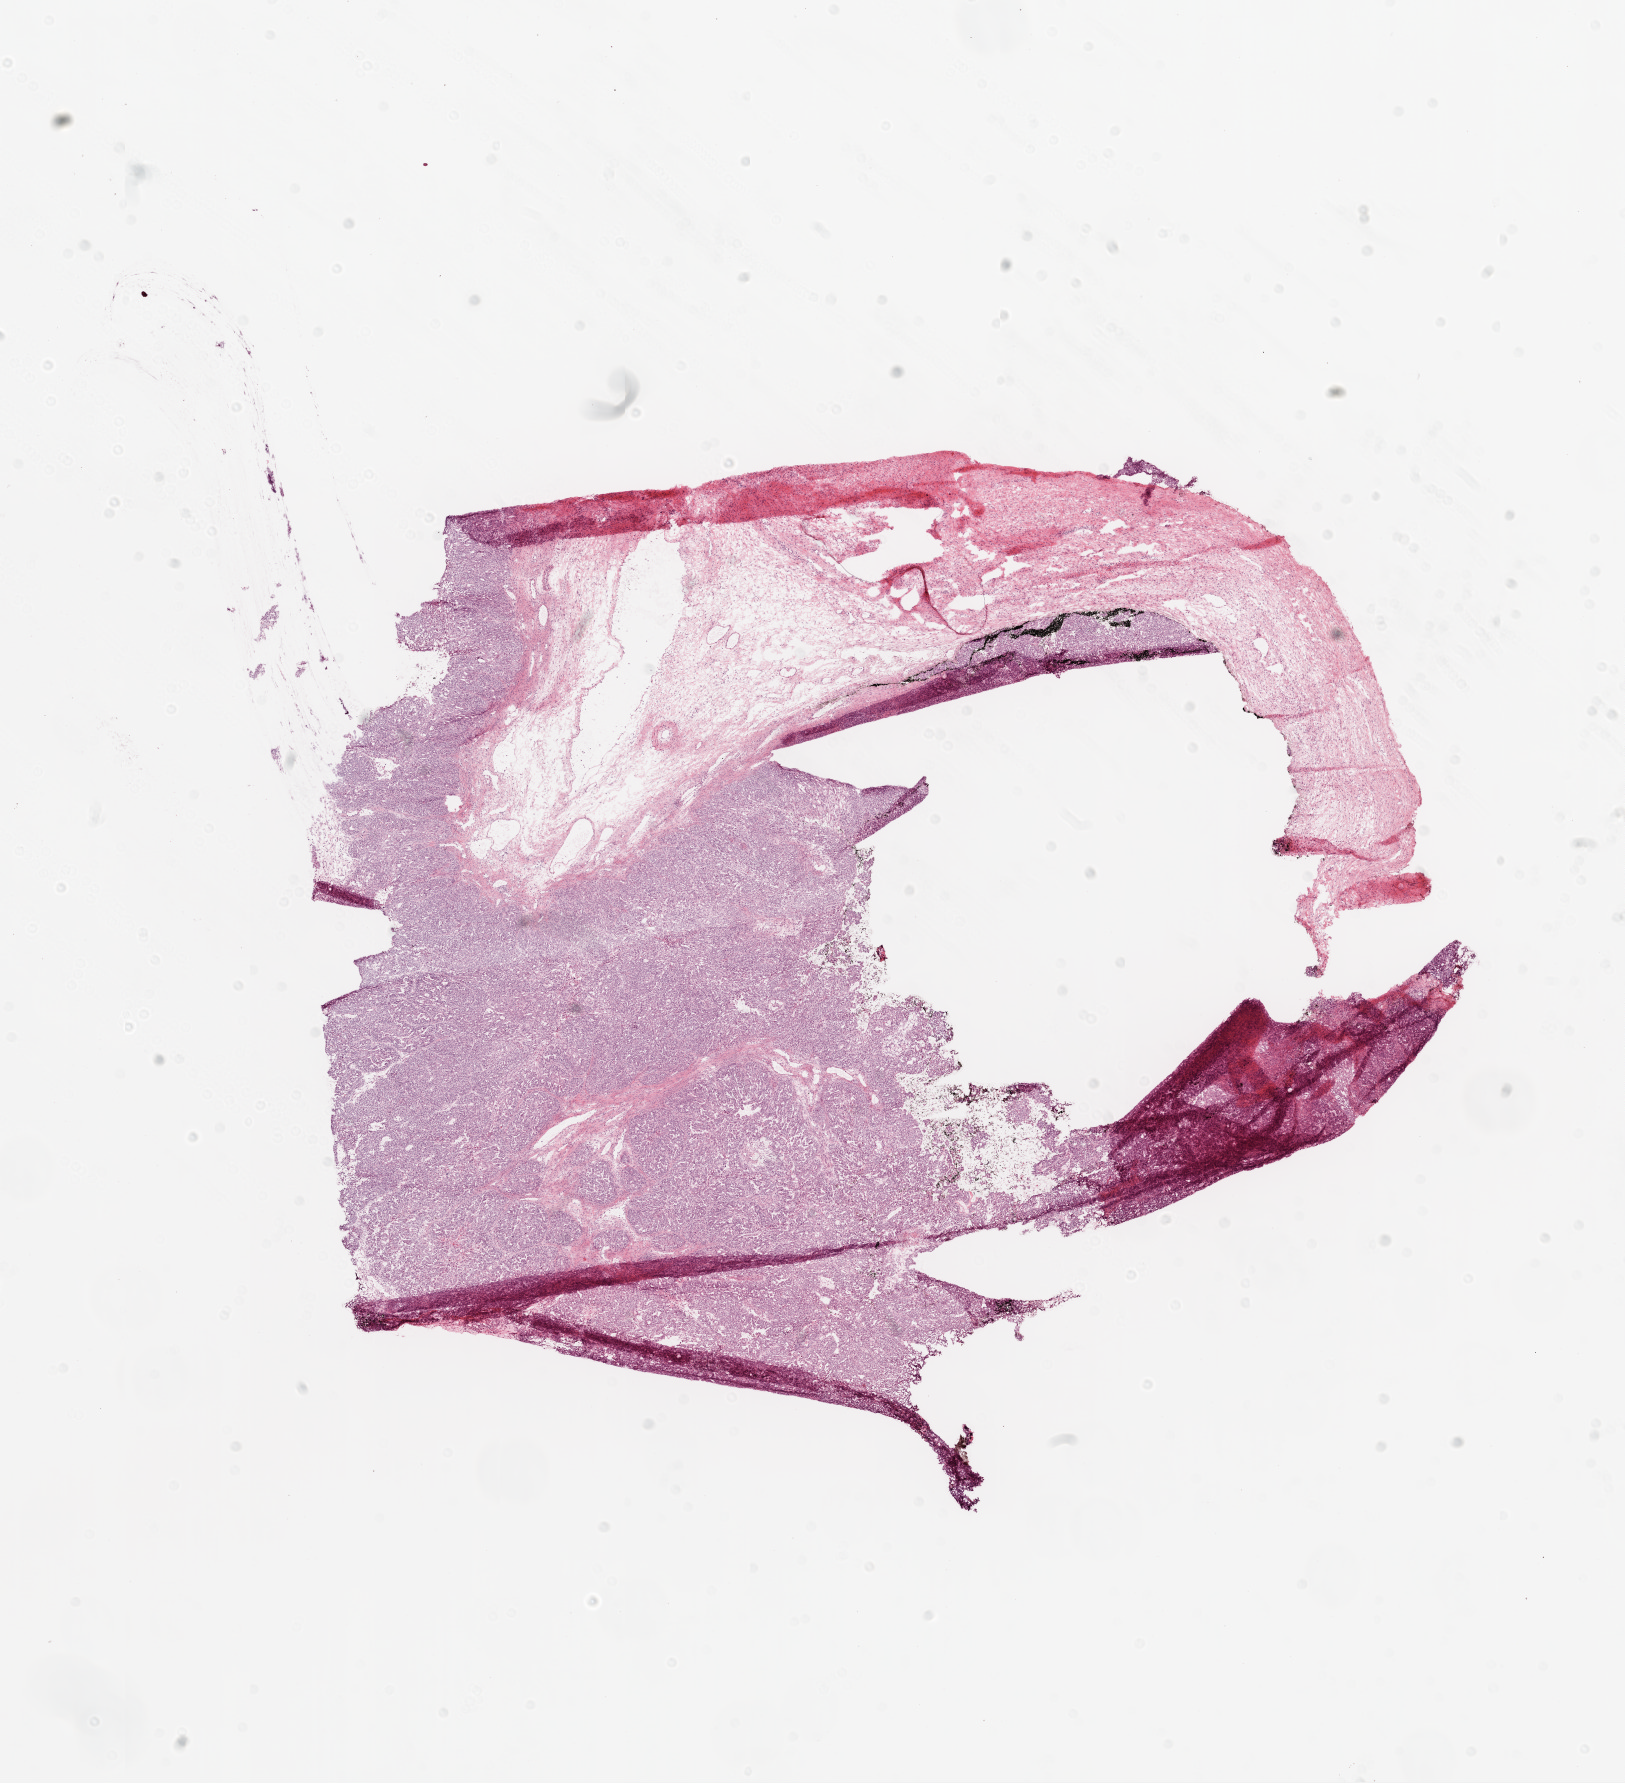
Digitized H&E tissue section (whole slide) — shown as a low-resolution overview of the whole scanned area (about 13.0 x 14.3 mm, from a 20x scan); frozen section from the top of the tissue portion; sample: primary tumour, ovary. Female, age 63 years at initial diagnosis. Composition of this section per pathologist review: tumour cells 80%, tumour nuclei 90%, normal cells 0%, stromal cells 10%, necrosis 10%.
Diagnosis: Serous cystadenocarcinoma, NOS.